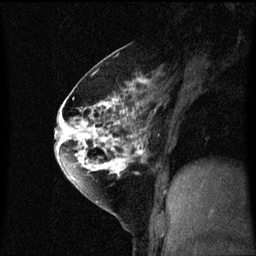
Breast MRI (dynamic contrast-enhanced), one sagittal slice; position 32 of 60 along the scan axis; dynamic contrast-enhanced series, image 2 of 3 at this slice position (ordered by acquisition); 1.5 T; TE 4.2 ms, TR 8.4 ms; 2 mm slice thickness; 256 × 256 image matrix, field of view 200 × 200 mm. Patient: female, 60 years.
Outlined on this slice (semi-automatic segmentation, software-assisted and operator-edited):
- analysis volume of interest (the breast-tissue region the enhancement analysis was run in; not a lesion): bounding box (x1, y1, x2, y2) in pixels: (64, 70, 145, 195)
- tumour enhancement mask (voxels above the 70 % enhancement threshold inside the analysis volume of interest): (64, 76, 145, 189)